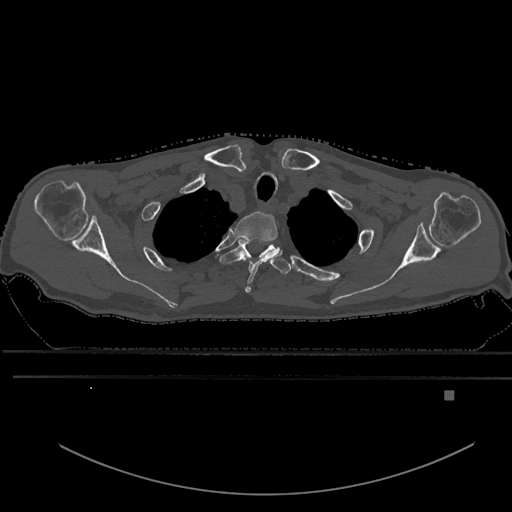
CT including the spine, one axial slice; position 512 of 969 along the scan axis; bone window (W 1800 / L 400 HU); 0.5 mm slice thickness; 512 × 512 image matrix, field of view 456 × 456 mm. Male patient, age 82 years. Case-level facts recorded for this patient, not image findings: primary cancer: prostate; vertebrae with lytic lesions (as recorded): T11, T9, T8, T2.
Outlined on this slice (semi-automatic segmentation, software-assisted and operator-edited):
- T1 vertebra: bounding box [x1, y1, x2, y2] px = [234, 211, 278, 293]
- T2 vertebra: [220, 239, 290, 274]